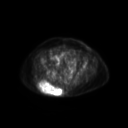
FDG PET of an extremity soft-tissue mass (from a PET/CT study), one axial slice. Slice 69 of 267 in the series (ordered by position). 3.27 mm slice thickness. 128 × 128 image matrix. Female patient, age 60 years. From the clinical record (not read from this slice): histological type: spindle cell suggestive of myxofibrosarcoma; grade: intermediate; site of the primary tumour: right buttock.
Outlined on this slice (expert contour drawn on MRI and transferred to this co-registered scan by the dataset authors):
- gross tumour volume (mass): bounding box [x1, y1, x2, y2] px = [37, 80, 63, 96]